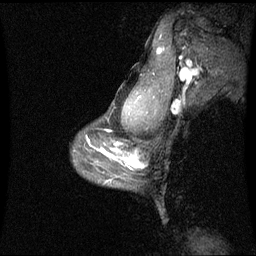
Breast MRI (dynamic contrast-enhanced), one sagittal slice. Slice 51 of 60 in the series (ordered by position). Dynamic contrast-enhanced series, image 2 of 3 at this slice position (ordered by acquisition). 1.5 T. TE 4.2 ms, TR 8.9 ms. 2 mm slice thickness. 256 × 256 image matrix, field of view 230 × 230 mm. Female patient, age 42 years. Case-level facts recorded for this patient, not image findings: setting: breast cancer imaged before/during neoadjuvant chemotherapy; receptor status: triple-negative.
Annotated regions visible in this slice (semi-automatic segmentation, software-assisted and operator-edited):
- analysis volume of interest (the breast-tissue region the enhancement analysis was run in; not a lesion): bounding box [x1, y1, x2, y2] px = [114, 150, 139, 179]
- tumour enhancement mask (voxels above the 70 % enhancement threshold inside the analysis volume of interest): [123, 158, 138, 167]